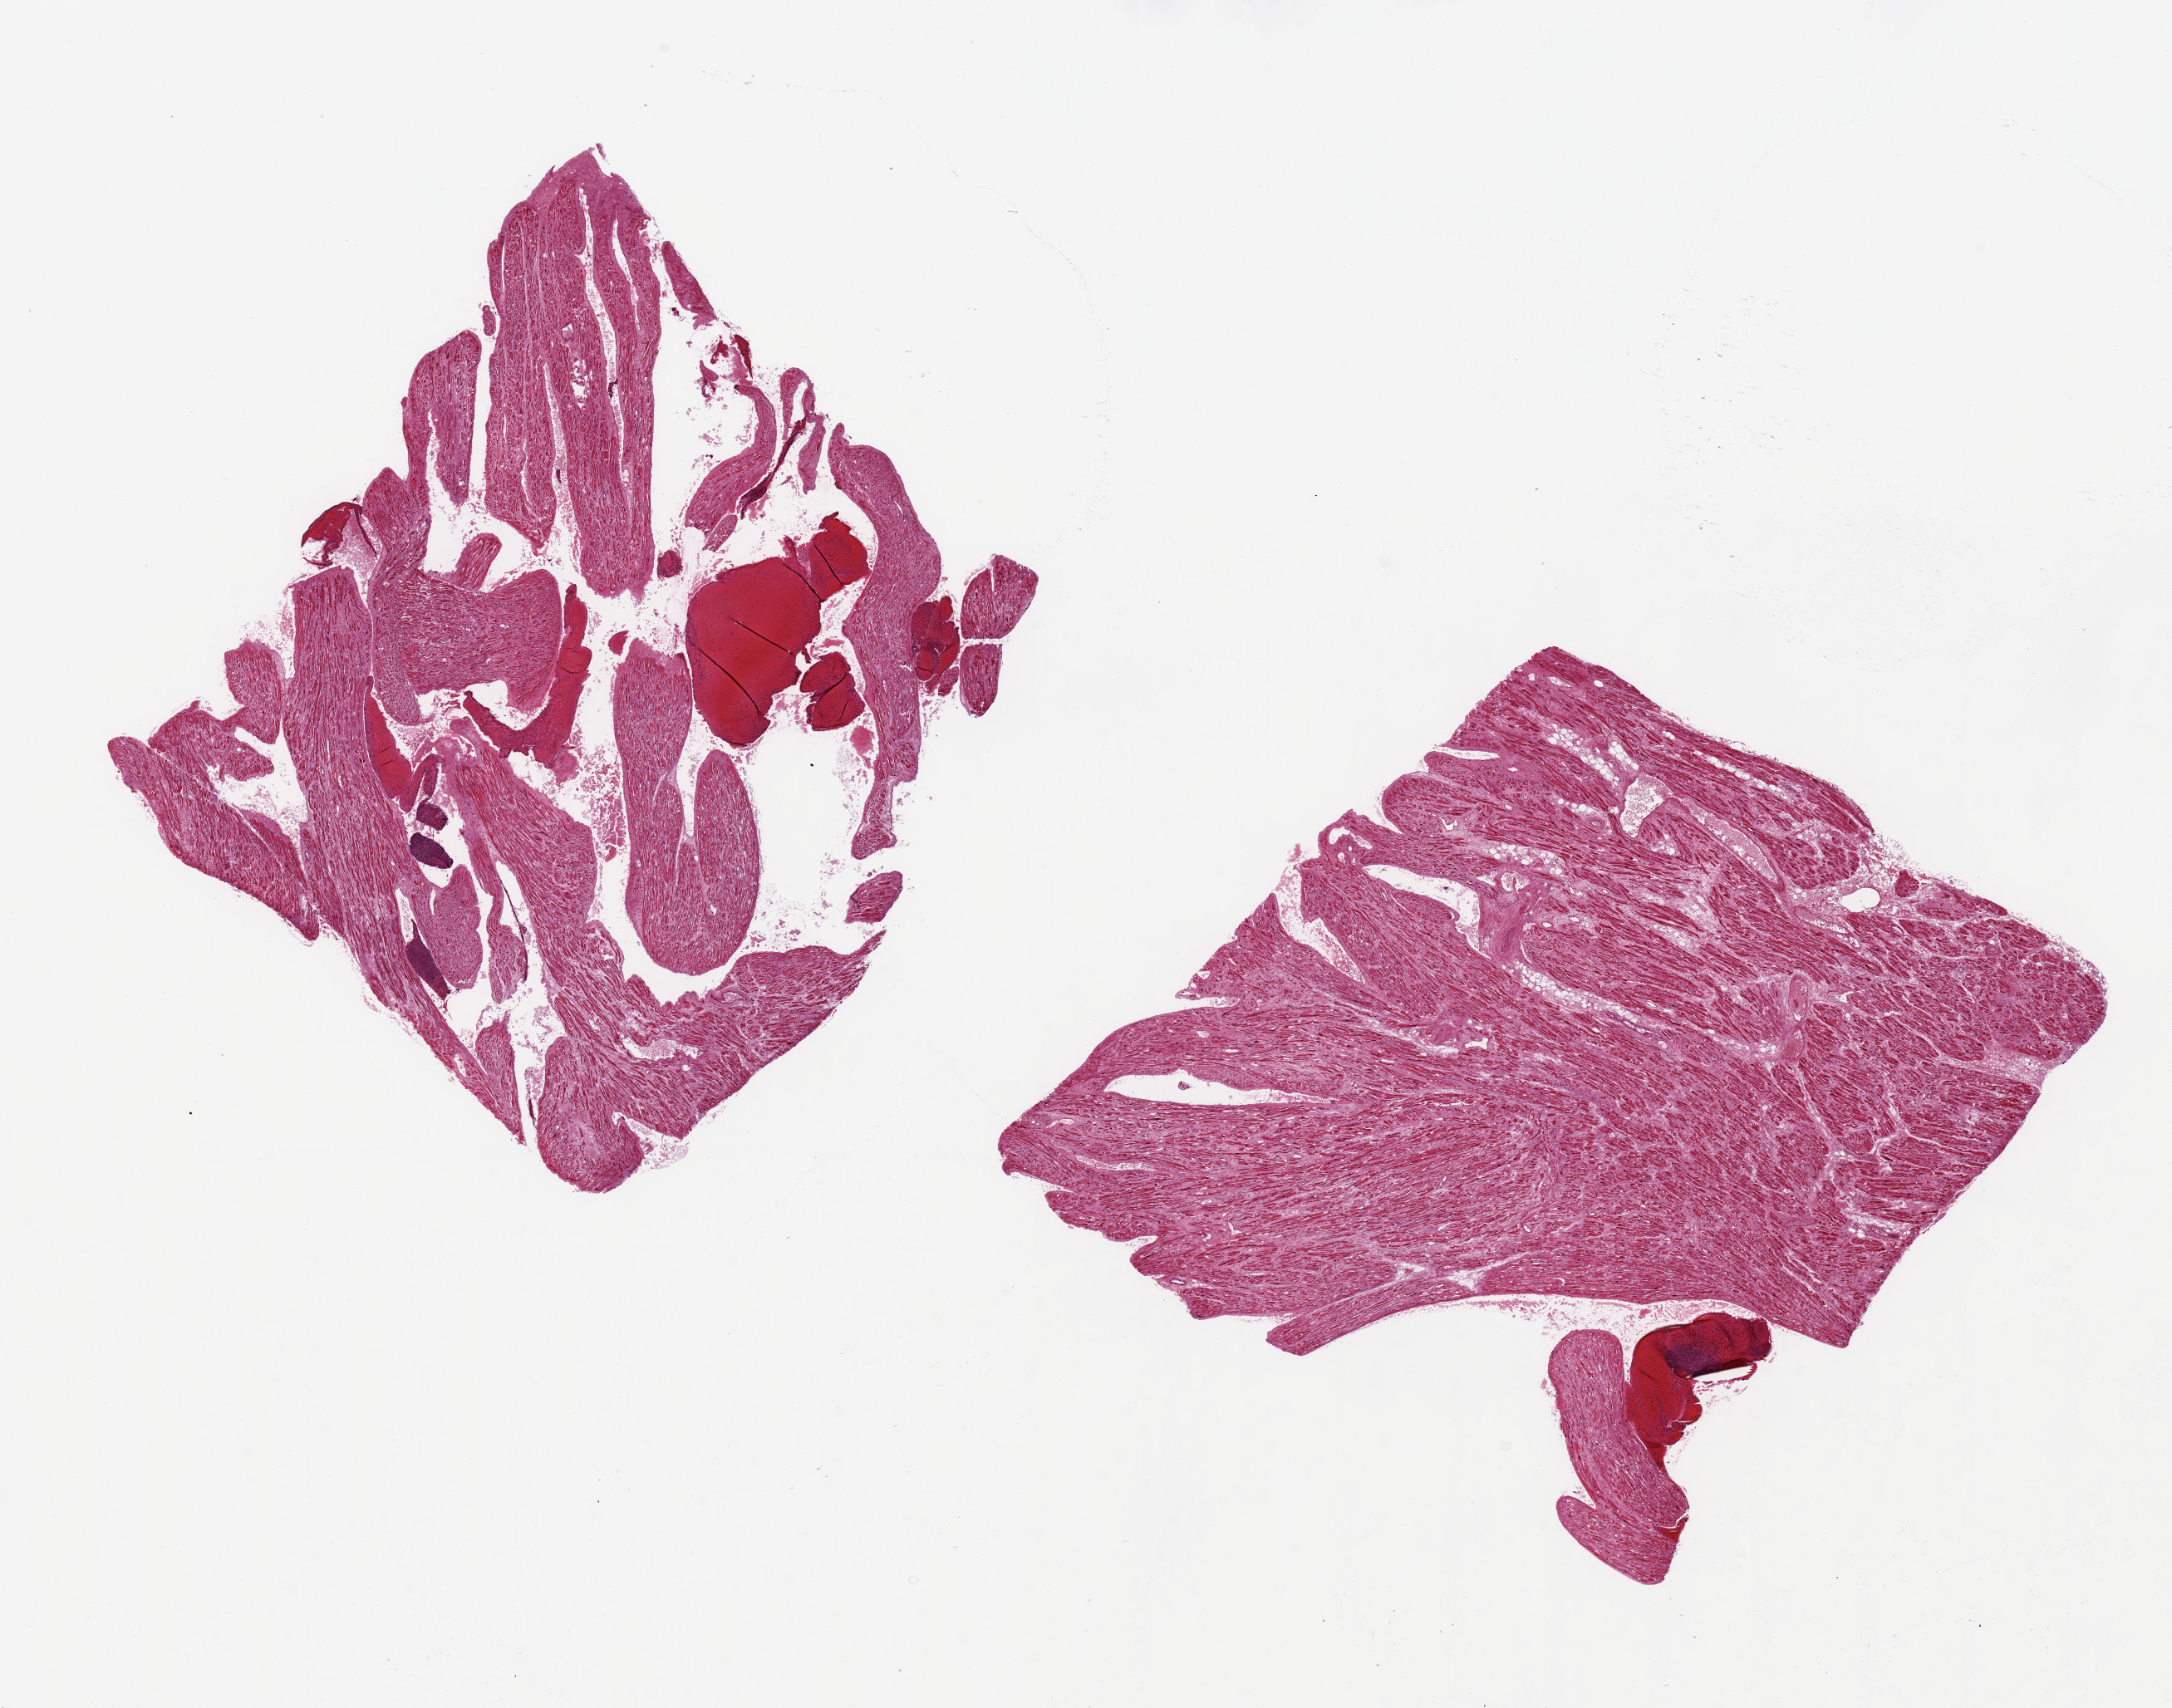
Digitized H&E-stained section, brightfield, shown as a low-resolution overview of the whole scanned area (about 20.7 x 16.3 mm, slide scanned at 20x). PAXgene-fixed, paraffin-embedded tissue. Section of auricular appendage (target tissue). Donor tissue sample. Donor sex: male.
* pathologist's review note for this sample: 2 pieces, 7.5x7 & 7x7mm; interstitial fibrosis; thrombi and clots in lumen